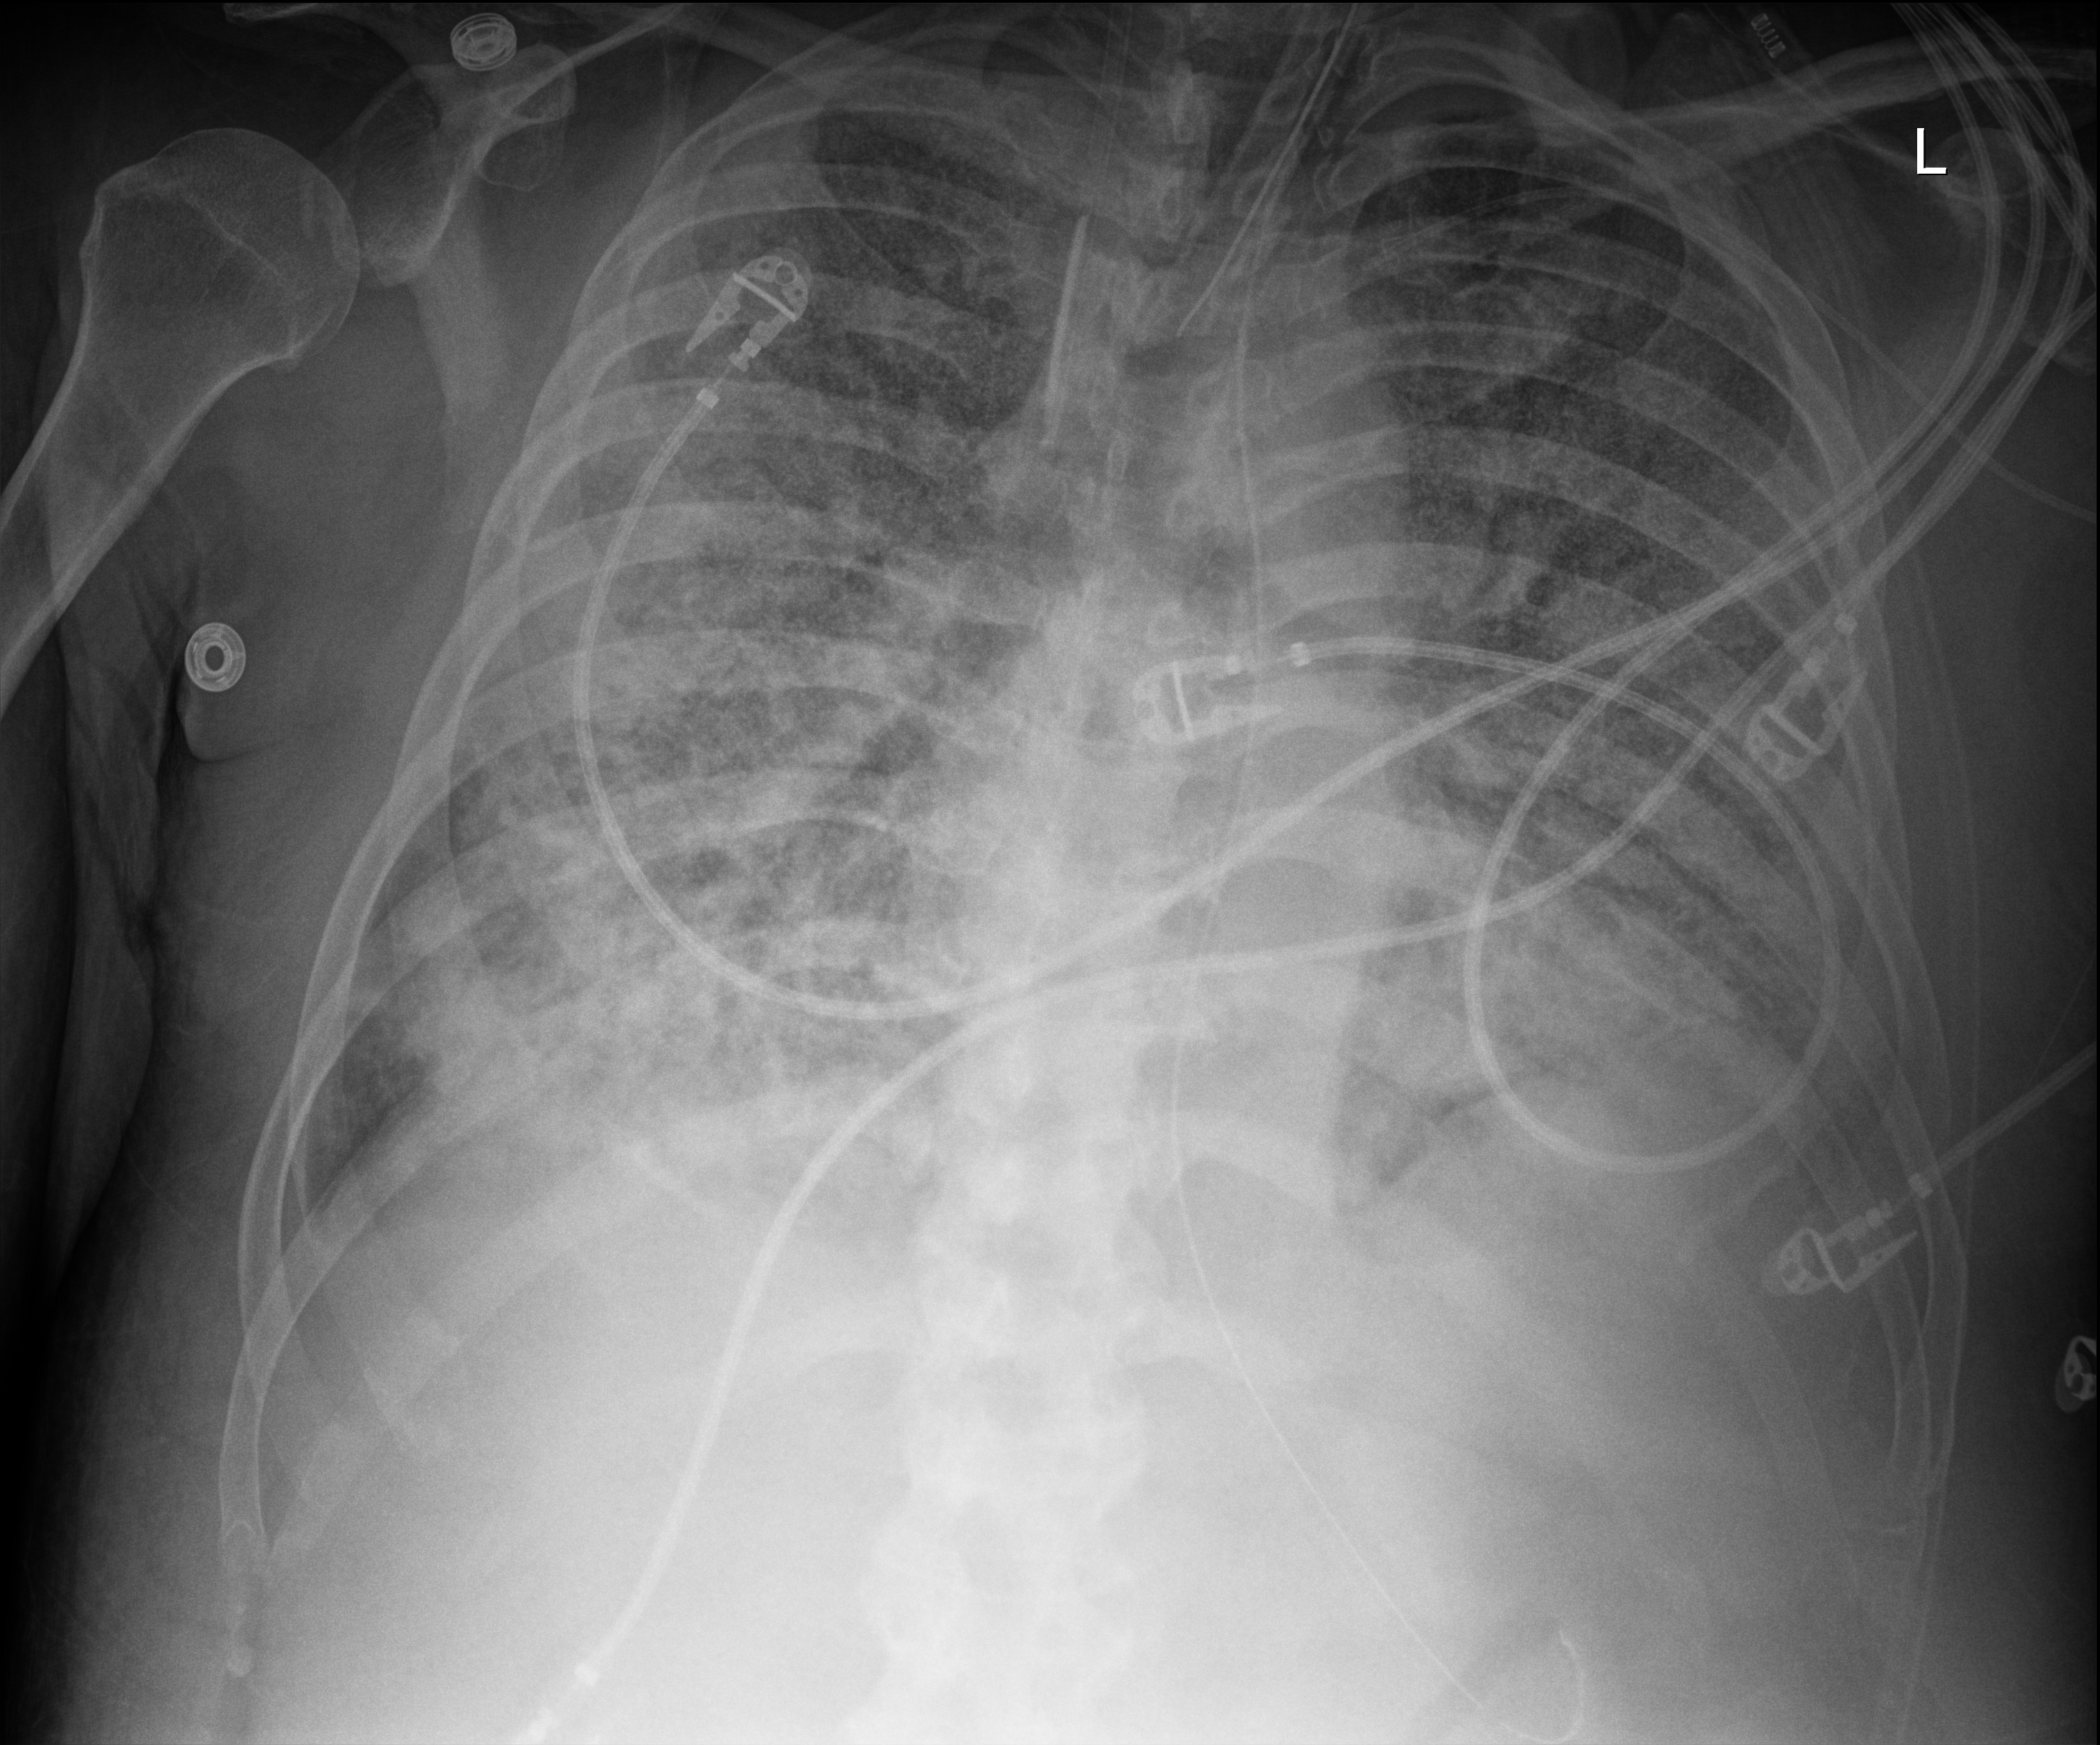
Bedside chest radiograph (digital radiography); anteroposterior (AP) projection. Patient hospitalised with COVID-19; male, aged 60–74 years.
From the hospital-stay record, not from the radiograph (when in the stay this image was taken is not recorded): COPD (admission record): no.